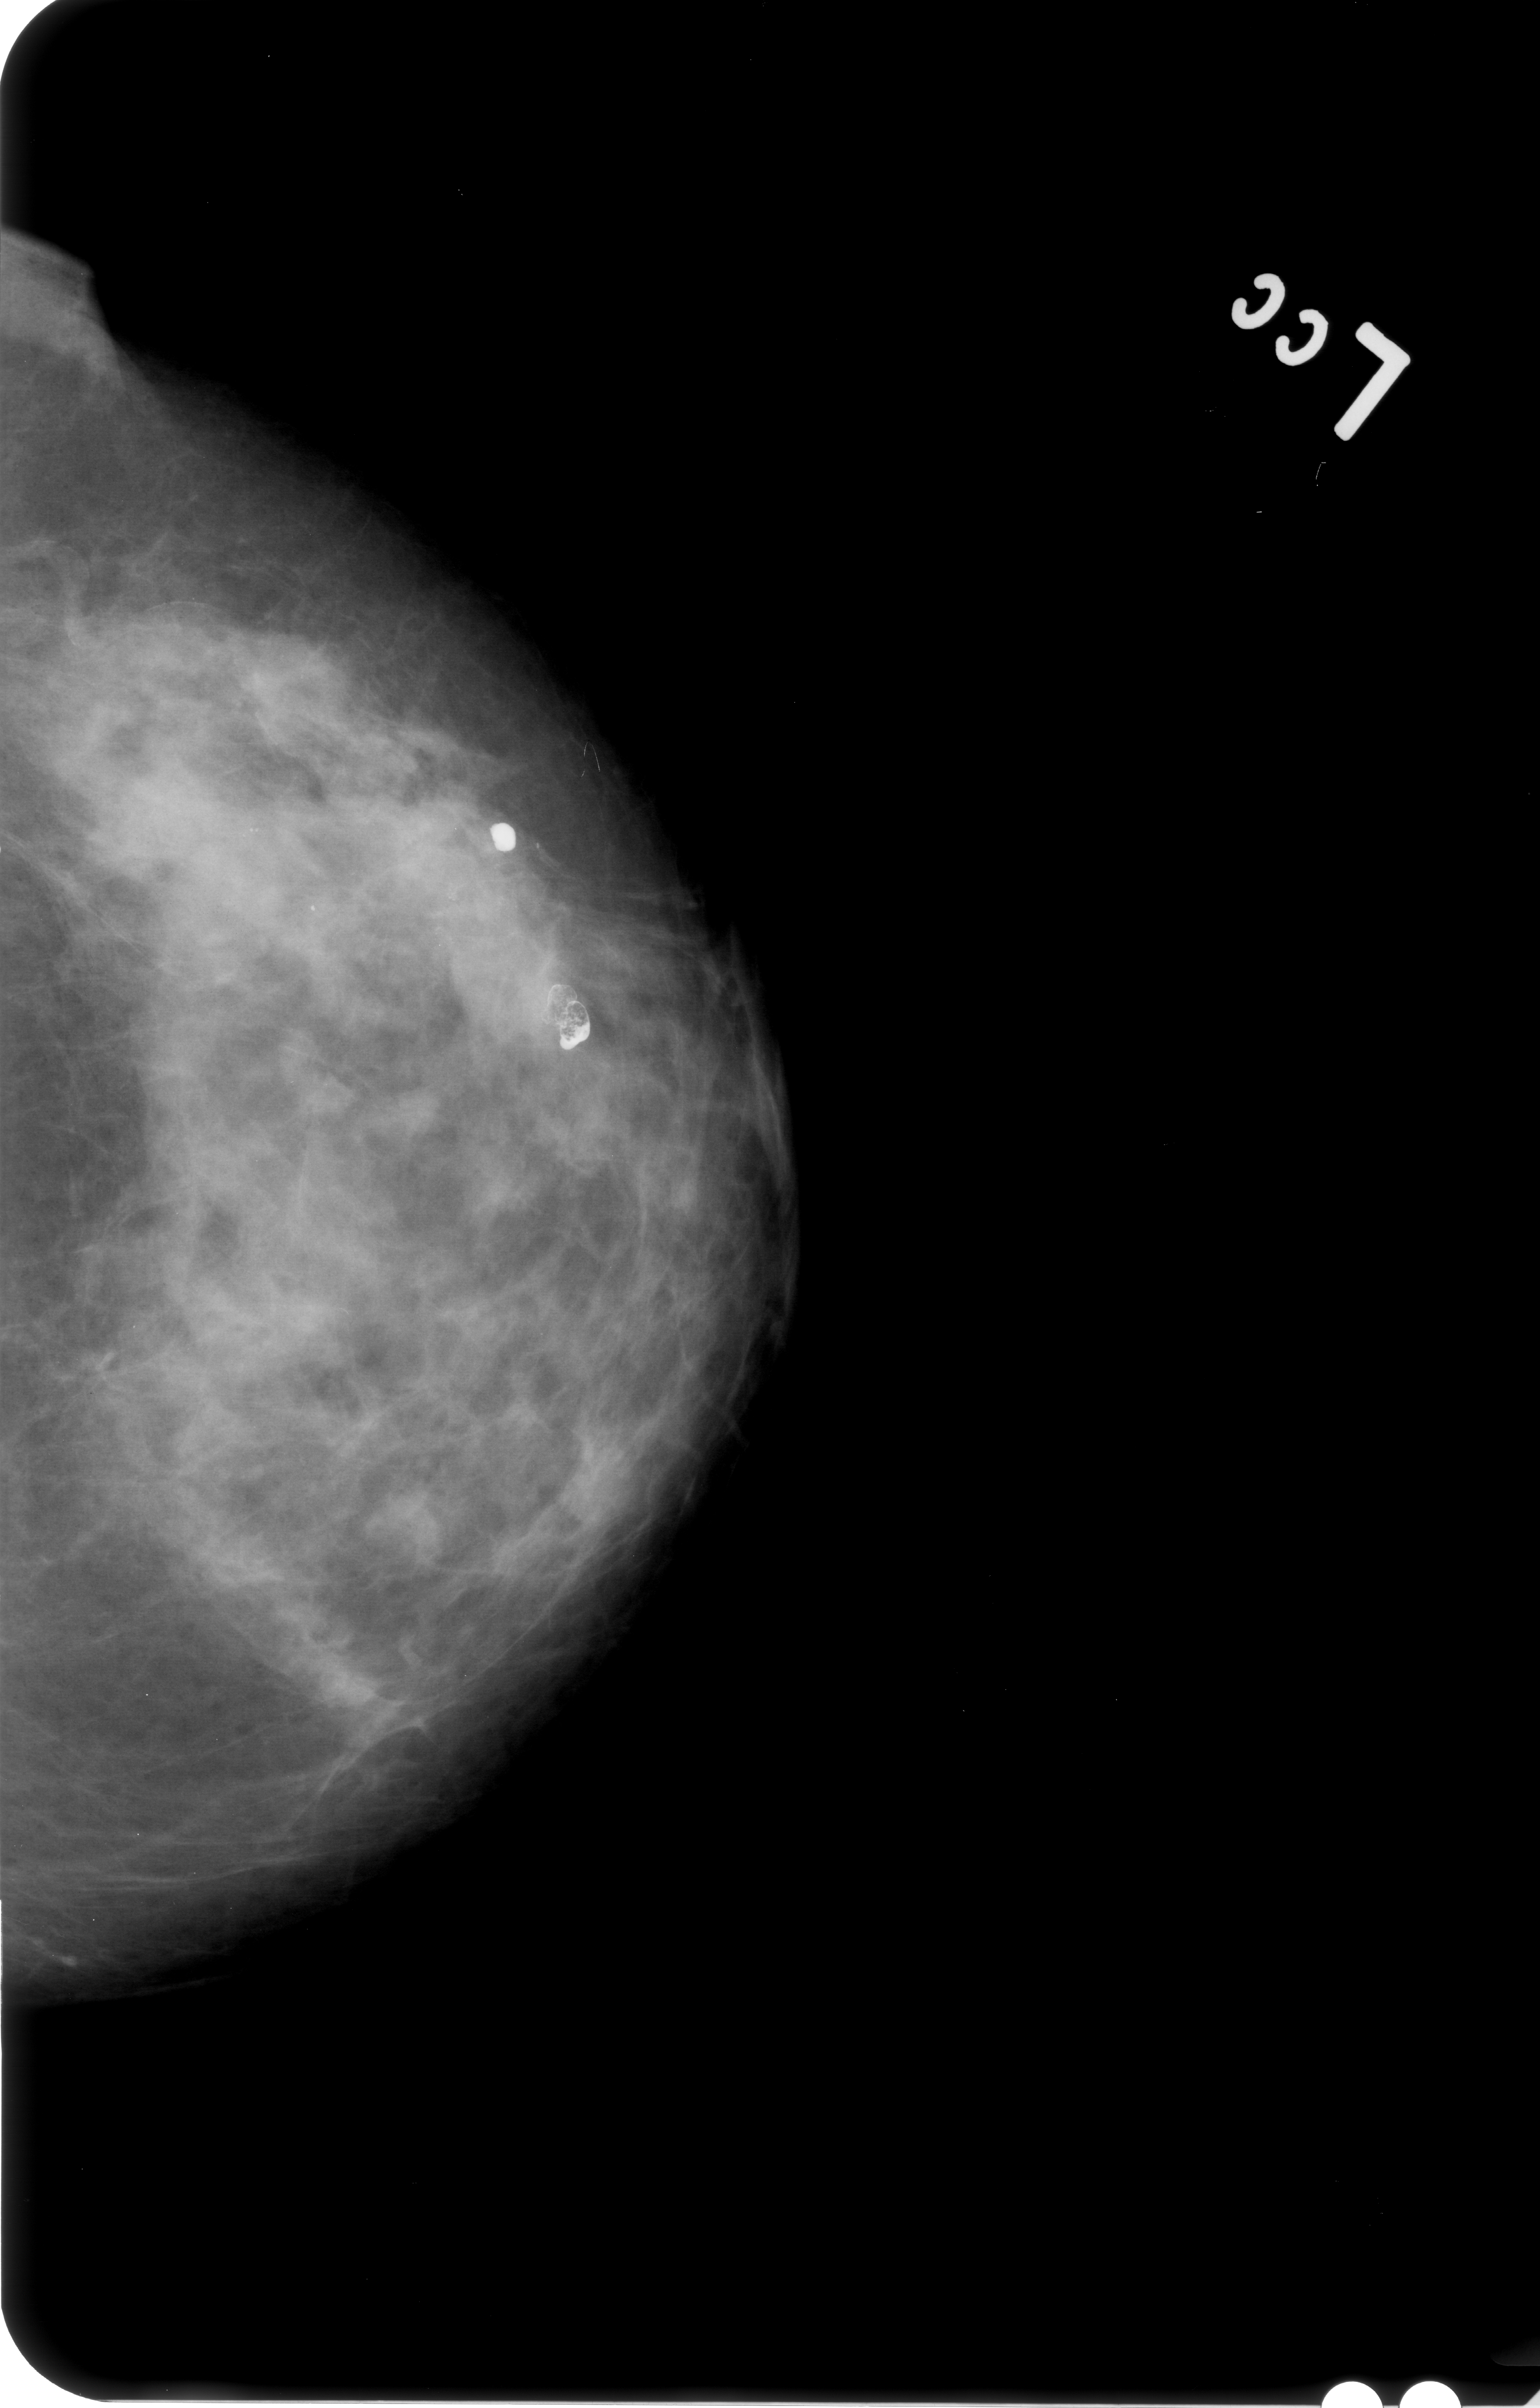
Scanned film-screen mammogram. Left breast. CC view. BI-RADS breast density category 3 (scale 1–4). 1540 × 2408 image matrix.
Expert-marked regions of interest on this film, with their recorded descriptors:
- calcifications, morphology punctate, distribution segmental; BI-RADS assessment category 4; pathology result (as recorded, not read from the image): malignant: box from (x=8, y=598) to (x=572, y=1058) px